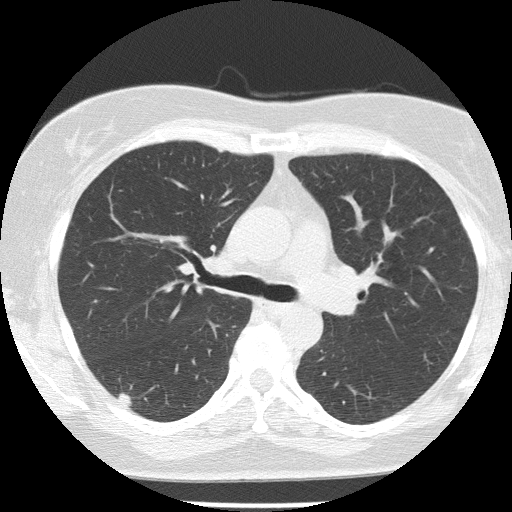
Axial slice from a low-dose chest CT screening exam, first (baseline) screen, lung window (W 1500 / L -600 HU), 2 mm slice thickness, slice 57 of 142 in the series. Female, age 58 years at enrolment.
• Expert-annotated lung lesion, bounding box <99,376,149,423> (left, top, right, bottom; pixels).
• The screening reader recorded 2 non-calcified nodules or masses ≥4 mm on this exam (right lower lobe, right lower lobe); which of them this box marks is not recorded.